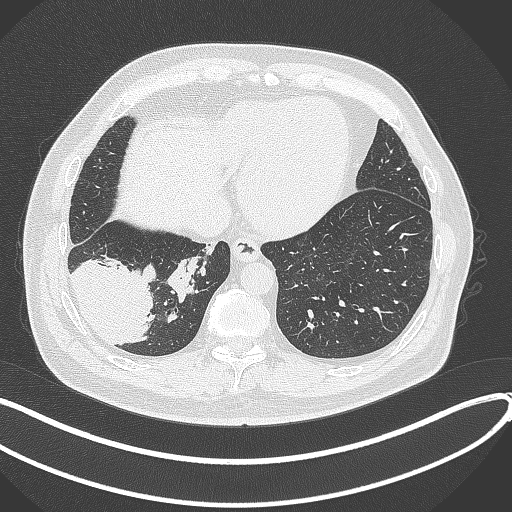
Chest CT, one axial slice; reconstruction kernel B70f; 120 kVp; lung window (W 1500 / L -600 HU); 1 mm slice thickness; 512 × 512 image matrix. Patient: male, 59 years.
Outlined on this slice (rectangle marked by the reading radiologist):
- lung tumour (recorded histology: adenocarcinoma): bounding box <69,256,164,348> (left, top, right, bottom; pixels)